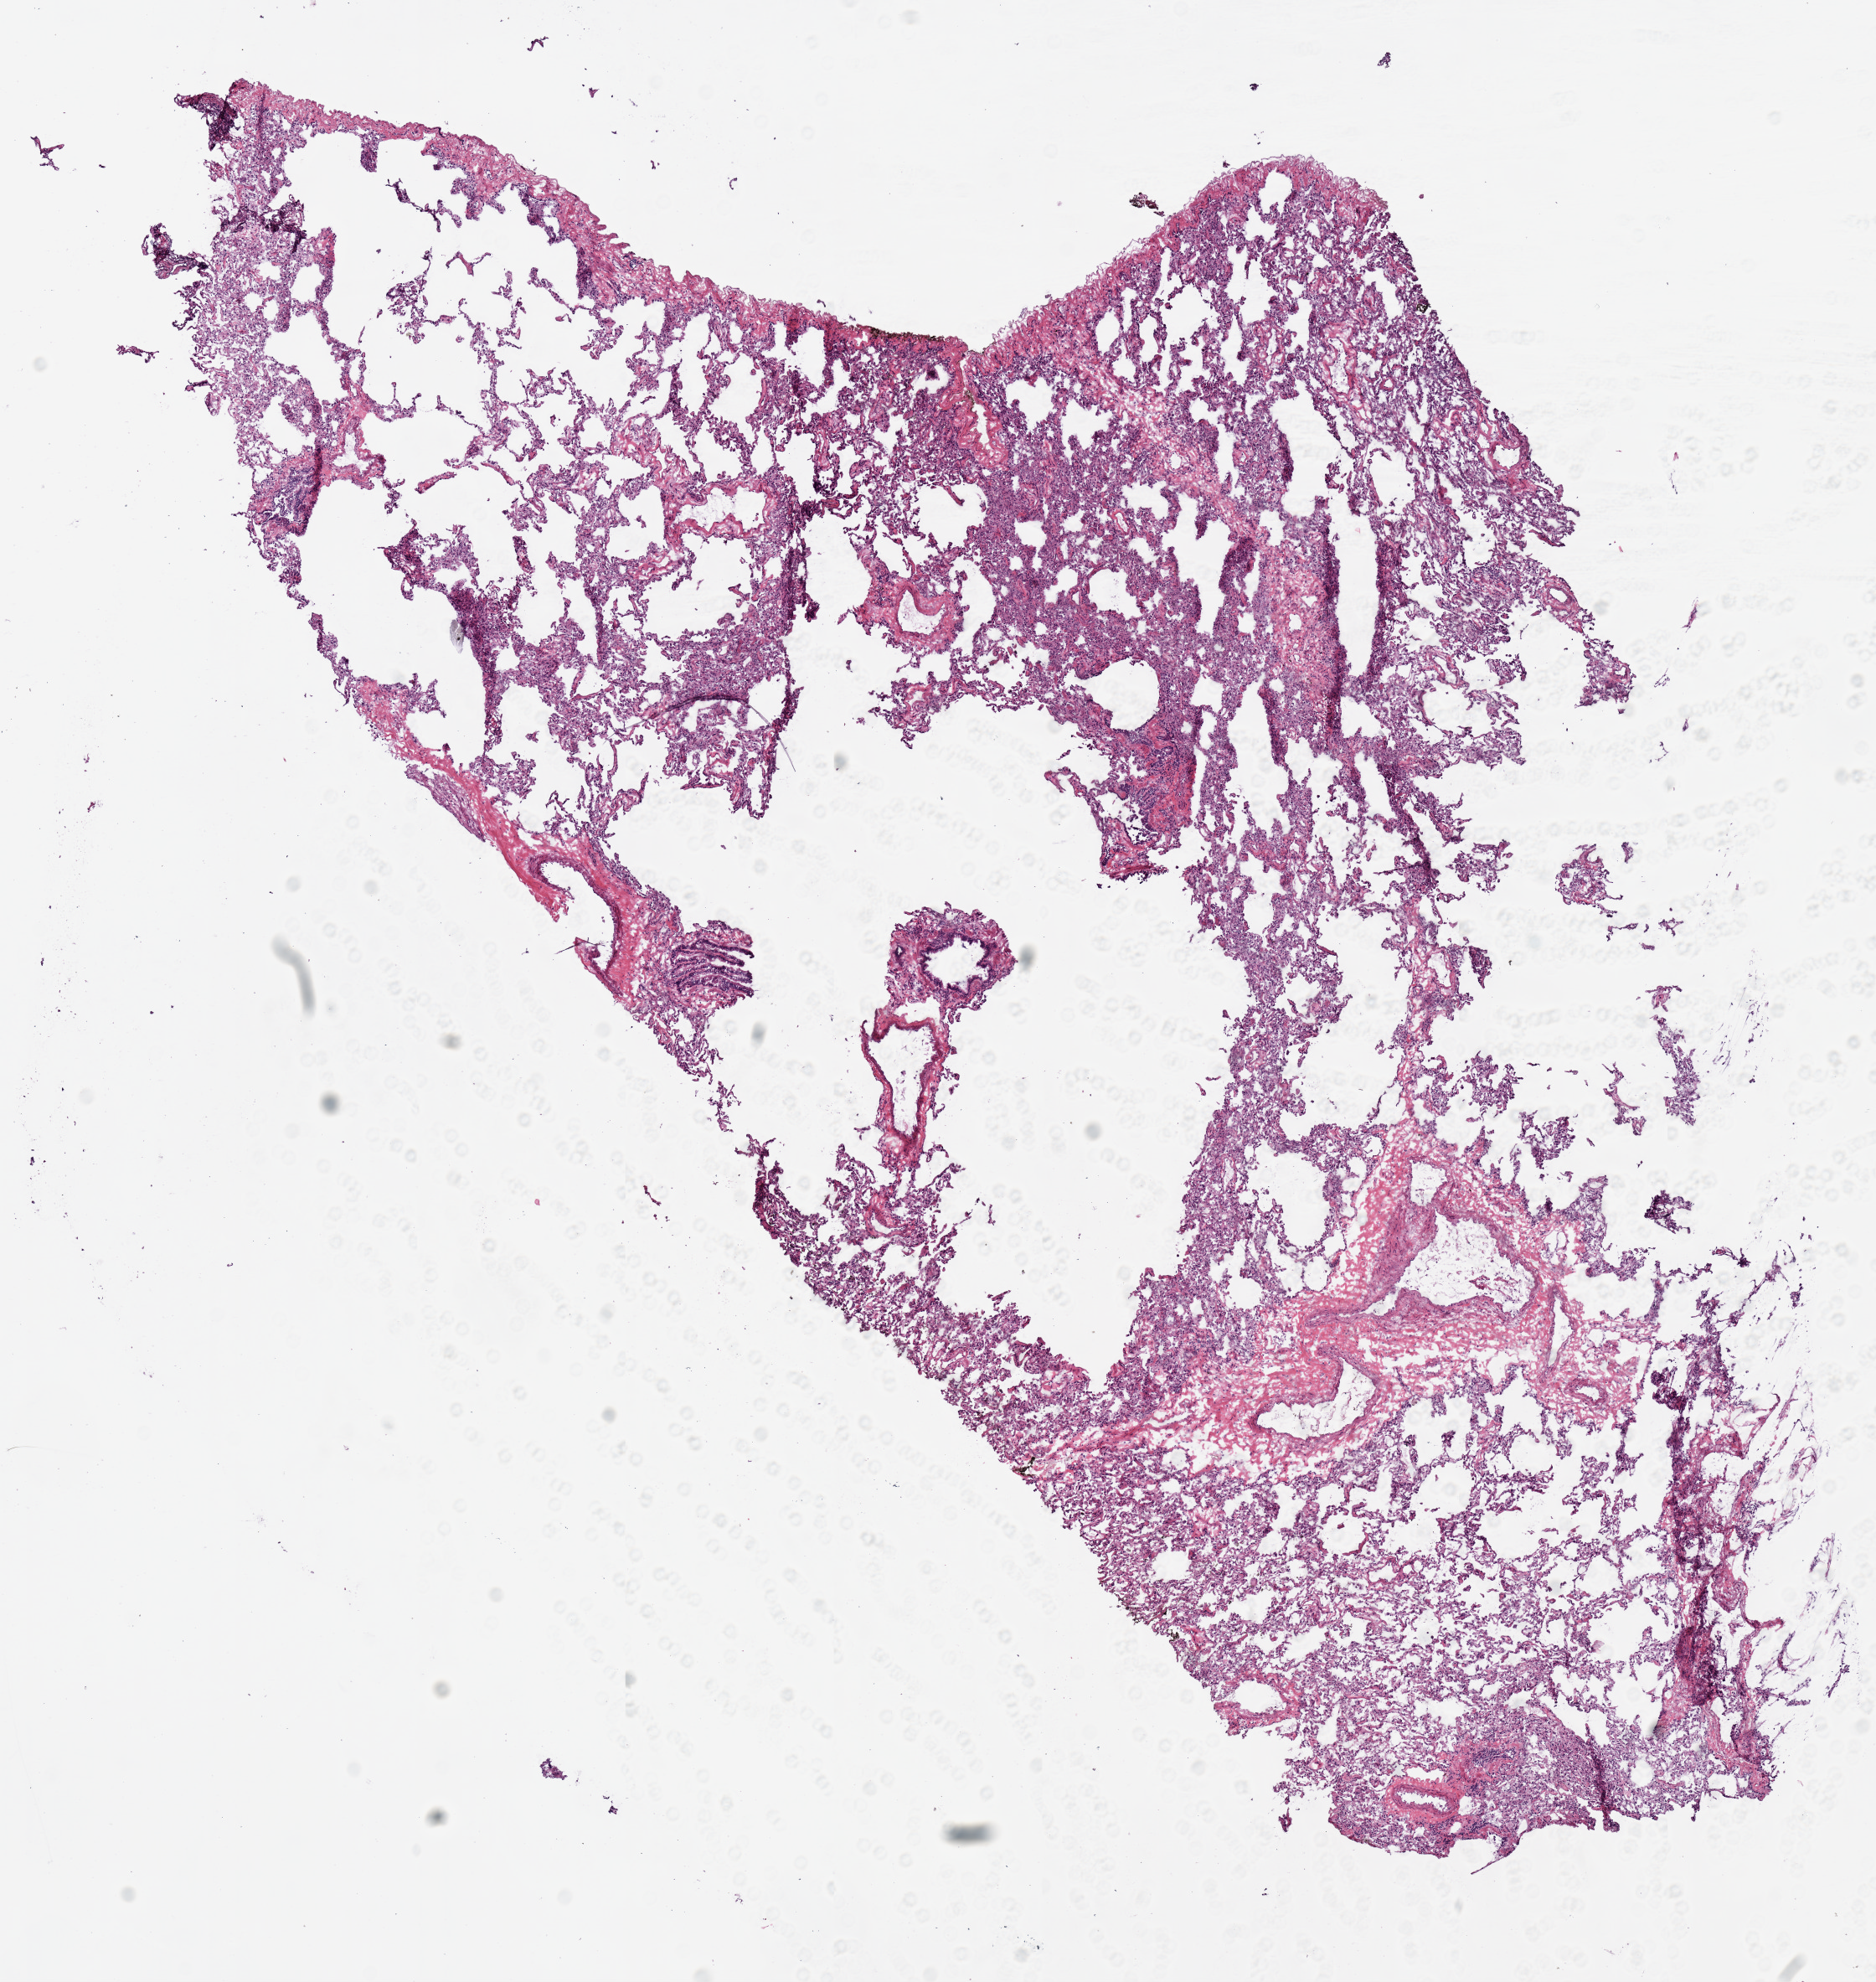
H&E whole-slide image, shown as a low-resolution overview of the whole scanned area (about 8.9 x 9.4 mm), frozen section from the top of the tissue portion, solid tissue normal (non-tumour tissue) sample from the lung. Male patient; age at initial diagnosis 56 years.
This section: solid tissue normal sample (biorepository sample class). Patient diagnosis: Bronchiolo-alveolar carcinoma, non-mucinous (lower lobe, lung).